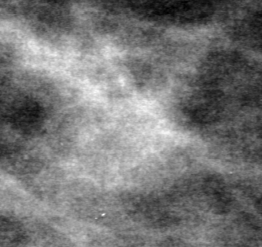
Cropped region of a digitized screen-film mammogram centred on a radiologist-marked abnormality, right breast, MLO view, BI-RADS breast density category 2 (scale 1–4).
Finding: mass, shape lobulated, margins circumscribed; BI-RADS assessment category 4; pathology result (as recorded, not read from the image): malignant.